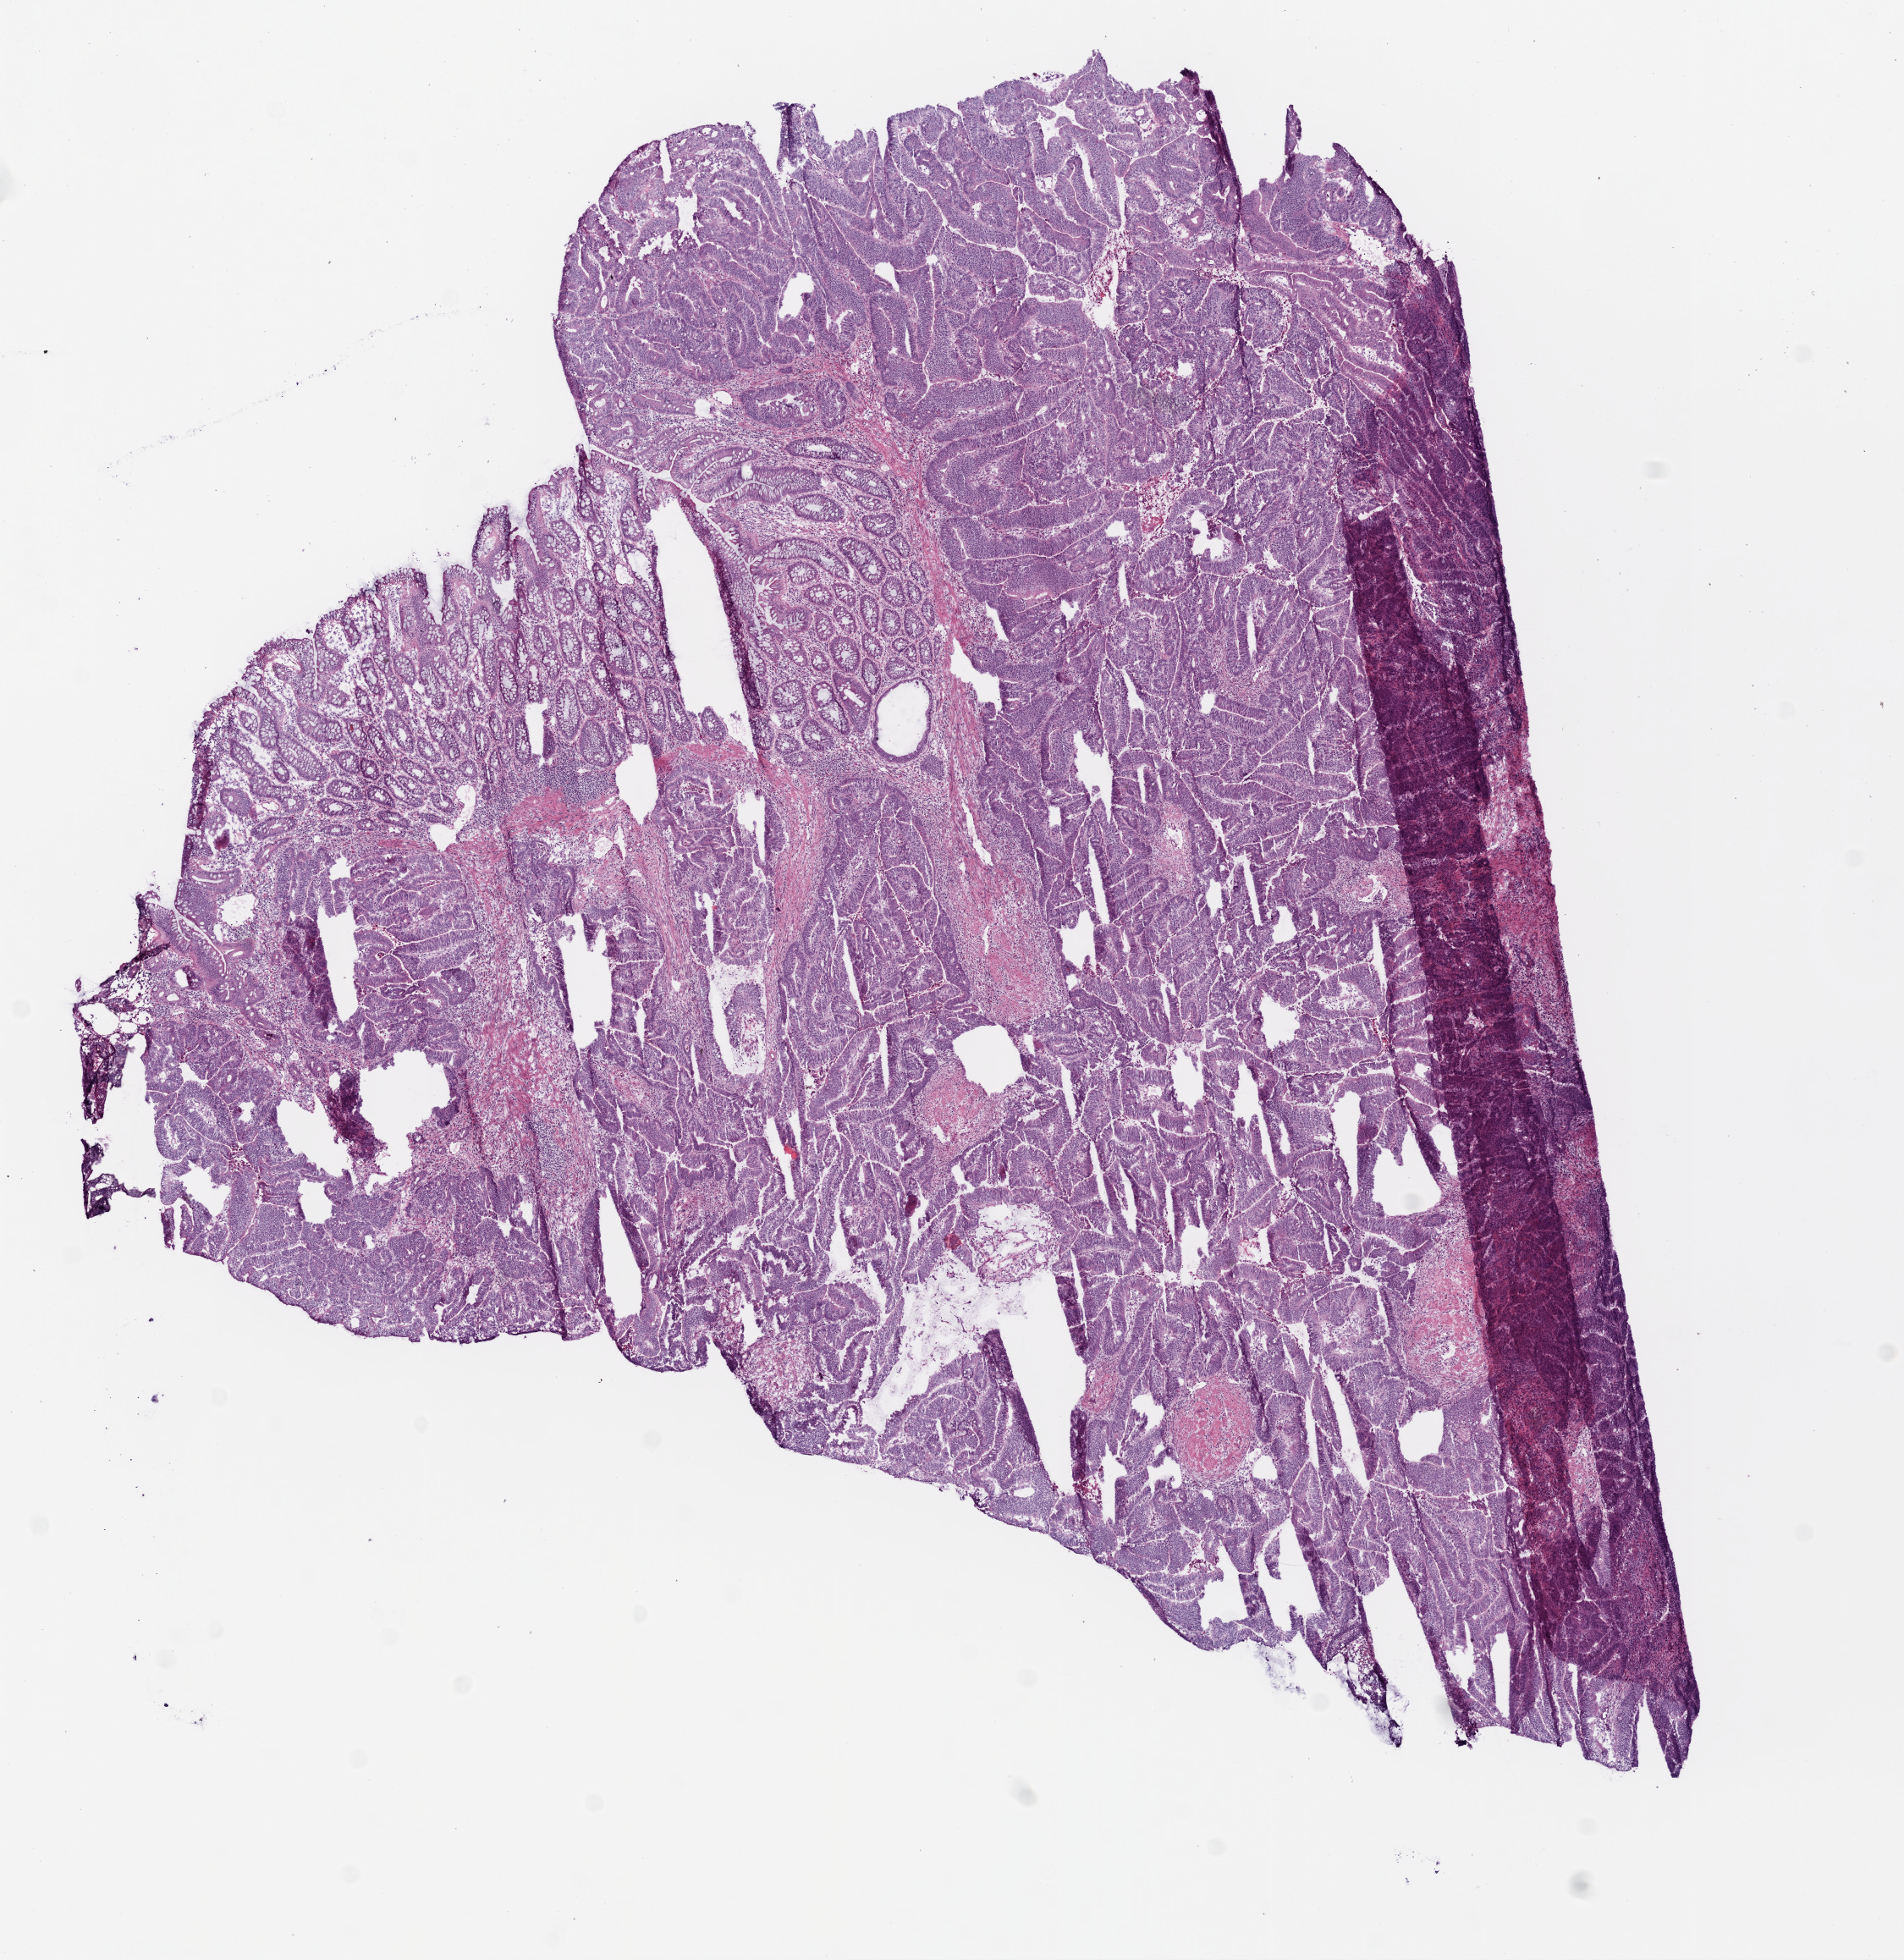
Digitized H&E tissue section (whole slide) — a low-resolution overview of the entire scanned area, about 9.0 x 9.3 mm (slide scanned at 20x); frozen section; primary tumour sample from the rectum. Male patient; age at initial diagnosis 70 years. Slide review estimates, as recorded: tumour cells 80%, tumour nuclei 80%, normal cells 15%, stromal cells 5%, necrosis 0%.
* diagnosis: Mucinous adenocarcinoma
* AJCC pathologic stage: I (5th edition)